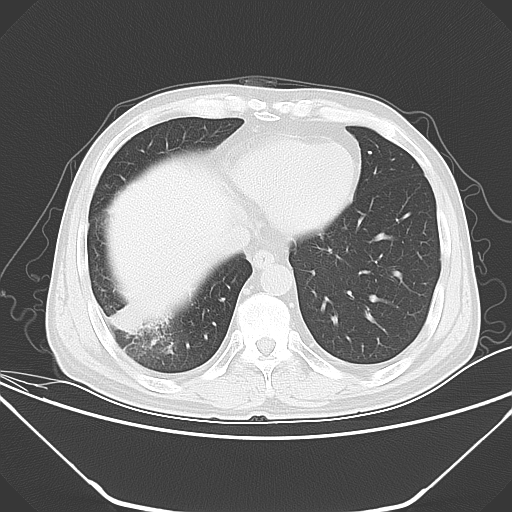
Chest CT, one axial slice; position 13 of 52 along the scan axis; 120 kVp; lung window (W 1500 / L -600 HU); 5 mm slice thickness; 512 × 512 image matrix, field of view 379 × 379 mm. Patient: male, 54 years. Case-level facts recorded for this patient, not image findings: clinical TNM (as recorded): T2 N1 M0; histopathological grade: G3.
Outlined on this slice (rectangle marked by the reading radiologist):
- lung tumour (recorded histology: adenocarcinoma): bounding box (x1, y1, x2, y2) in pixels: (105, 294, 144, 336)